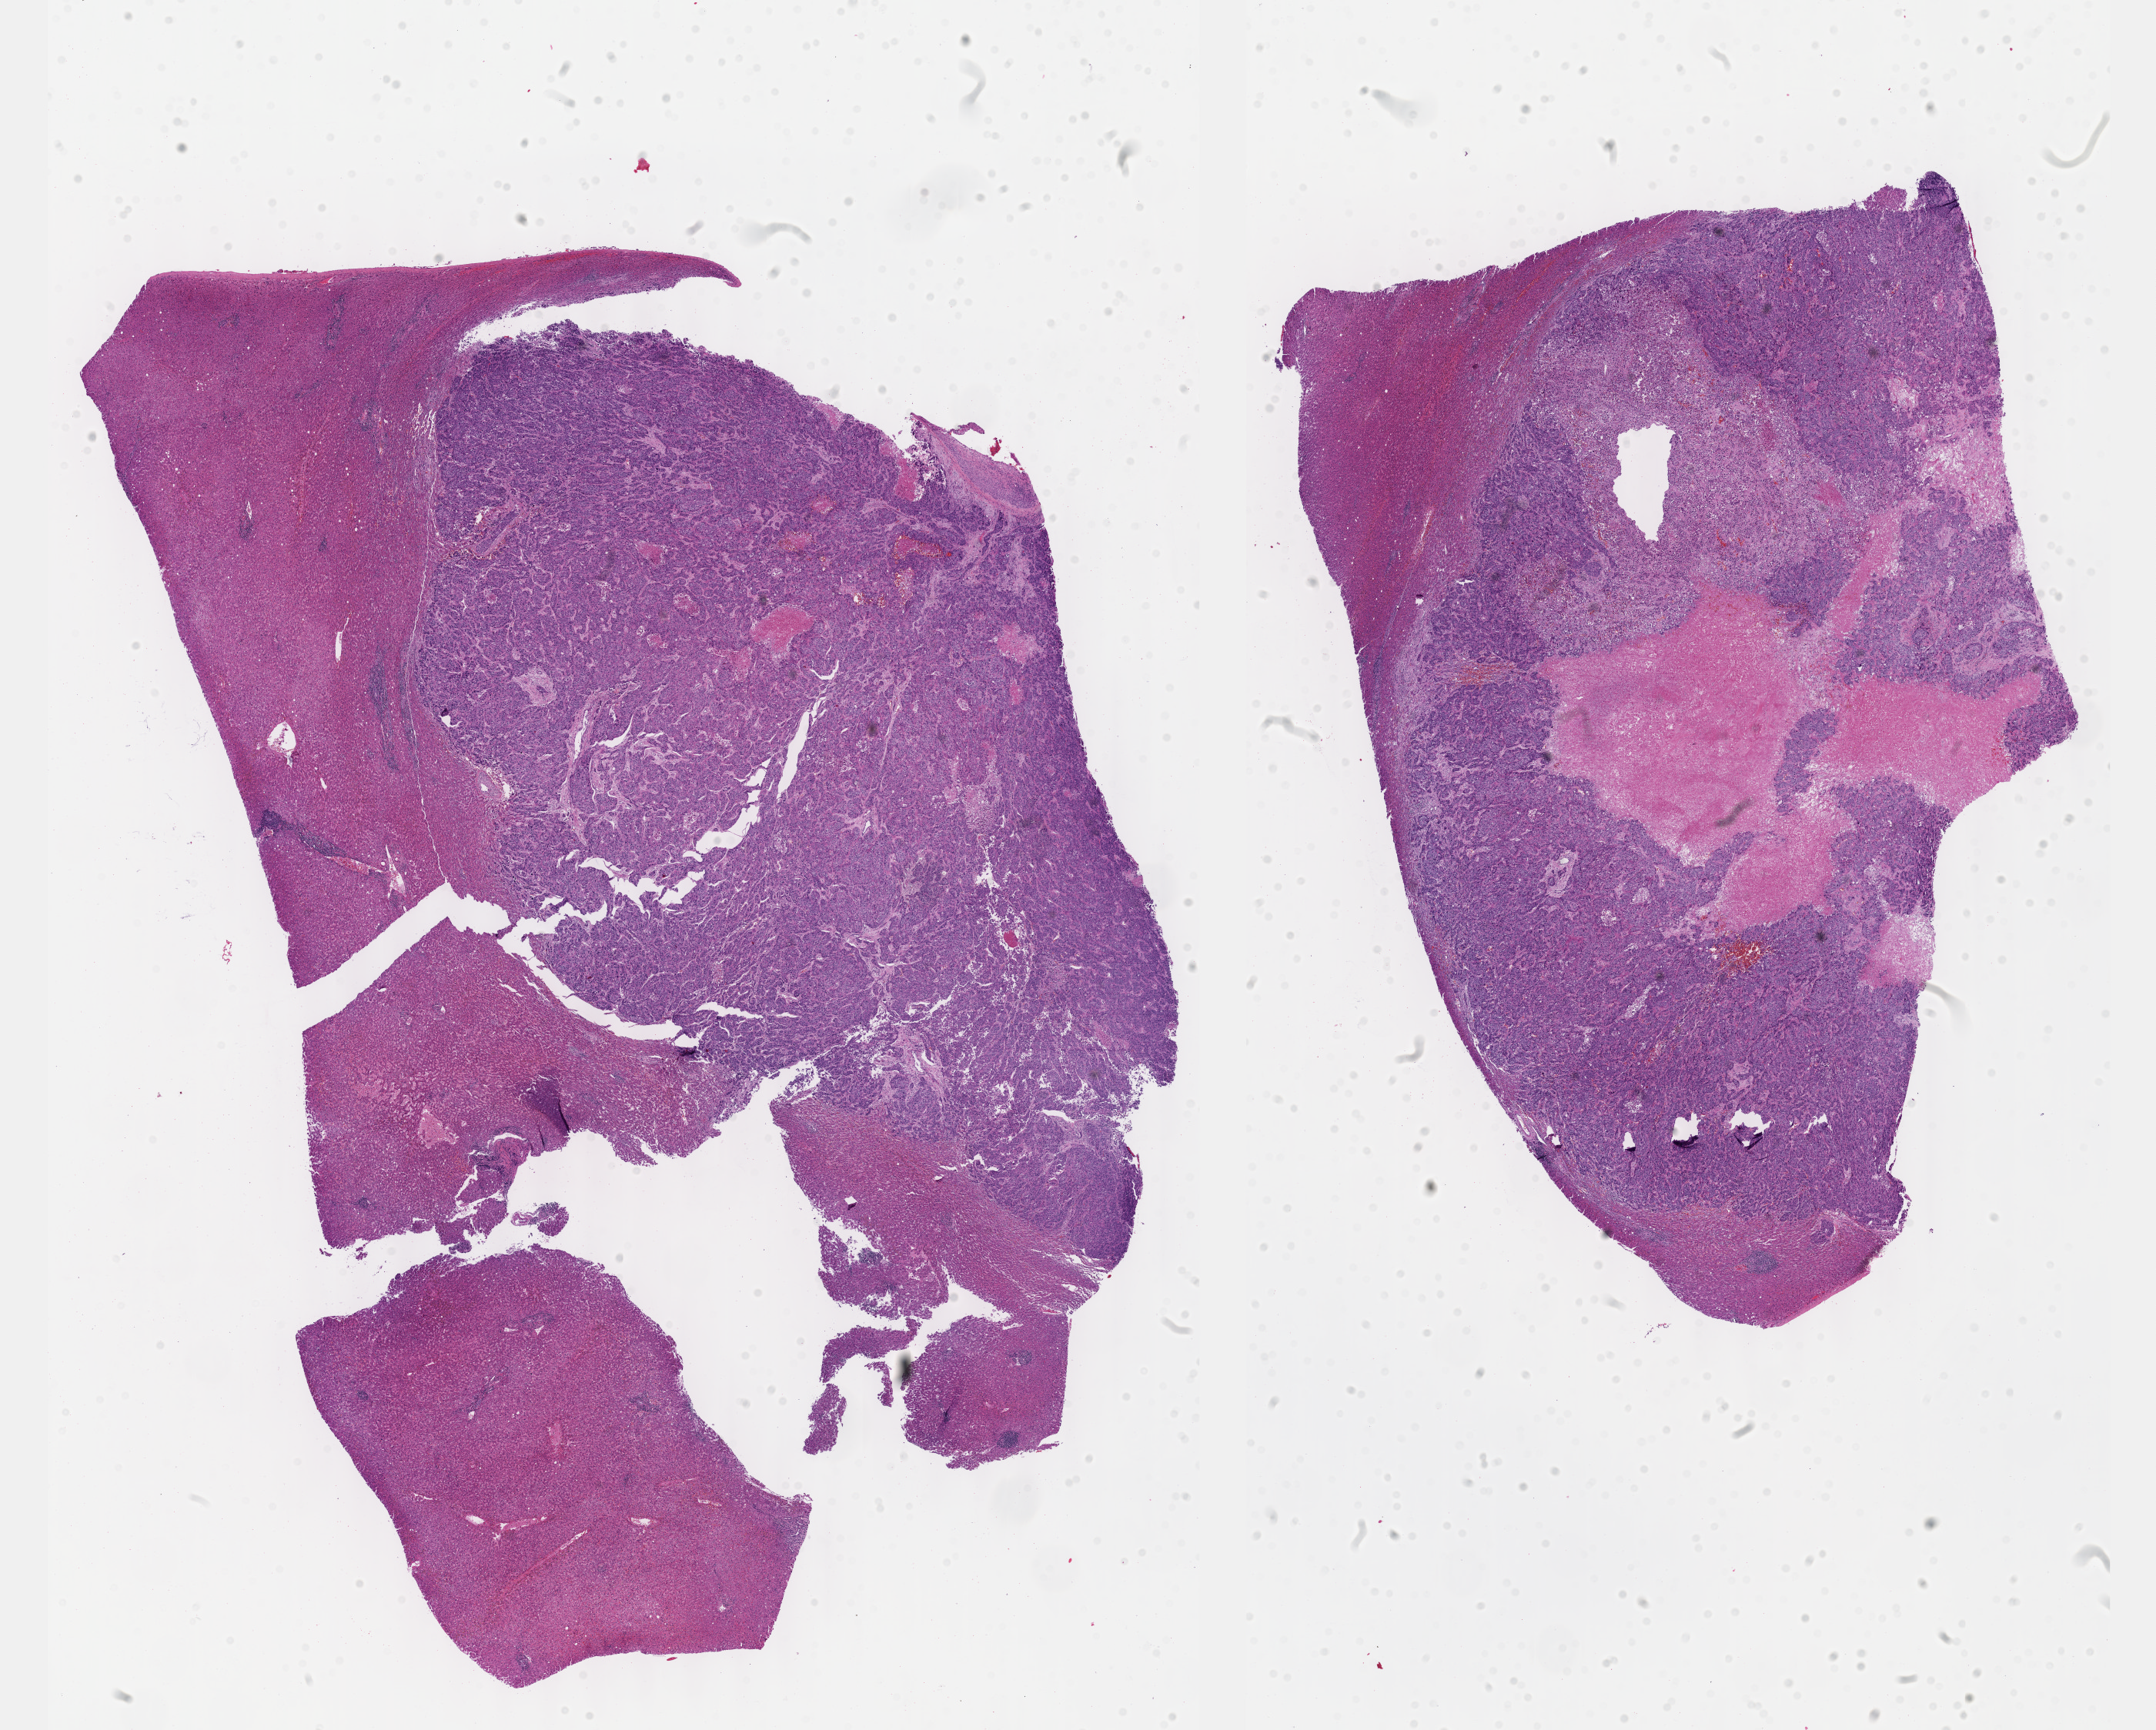
Digitized H&E tissue section (whole slide) — a low-resolution overview of the entire scanned area, about 22.6 x 18.2 mm (slide scanned at 40x); formalin-fixed paraffin-embedded (FFPE) diagnostic section; primary tumour sample from the liver. Female, age 71 years at initial diagnosis. Histologic grade: G3 (poorly differentiated).
Diagnosis: Hepatocellular carcinoma, NOS.